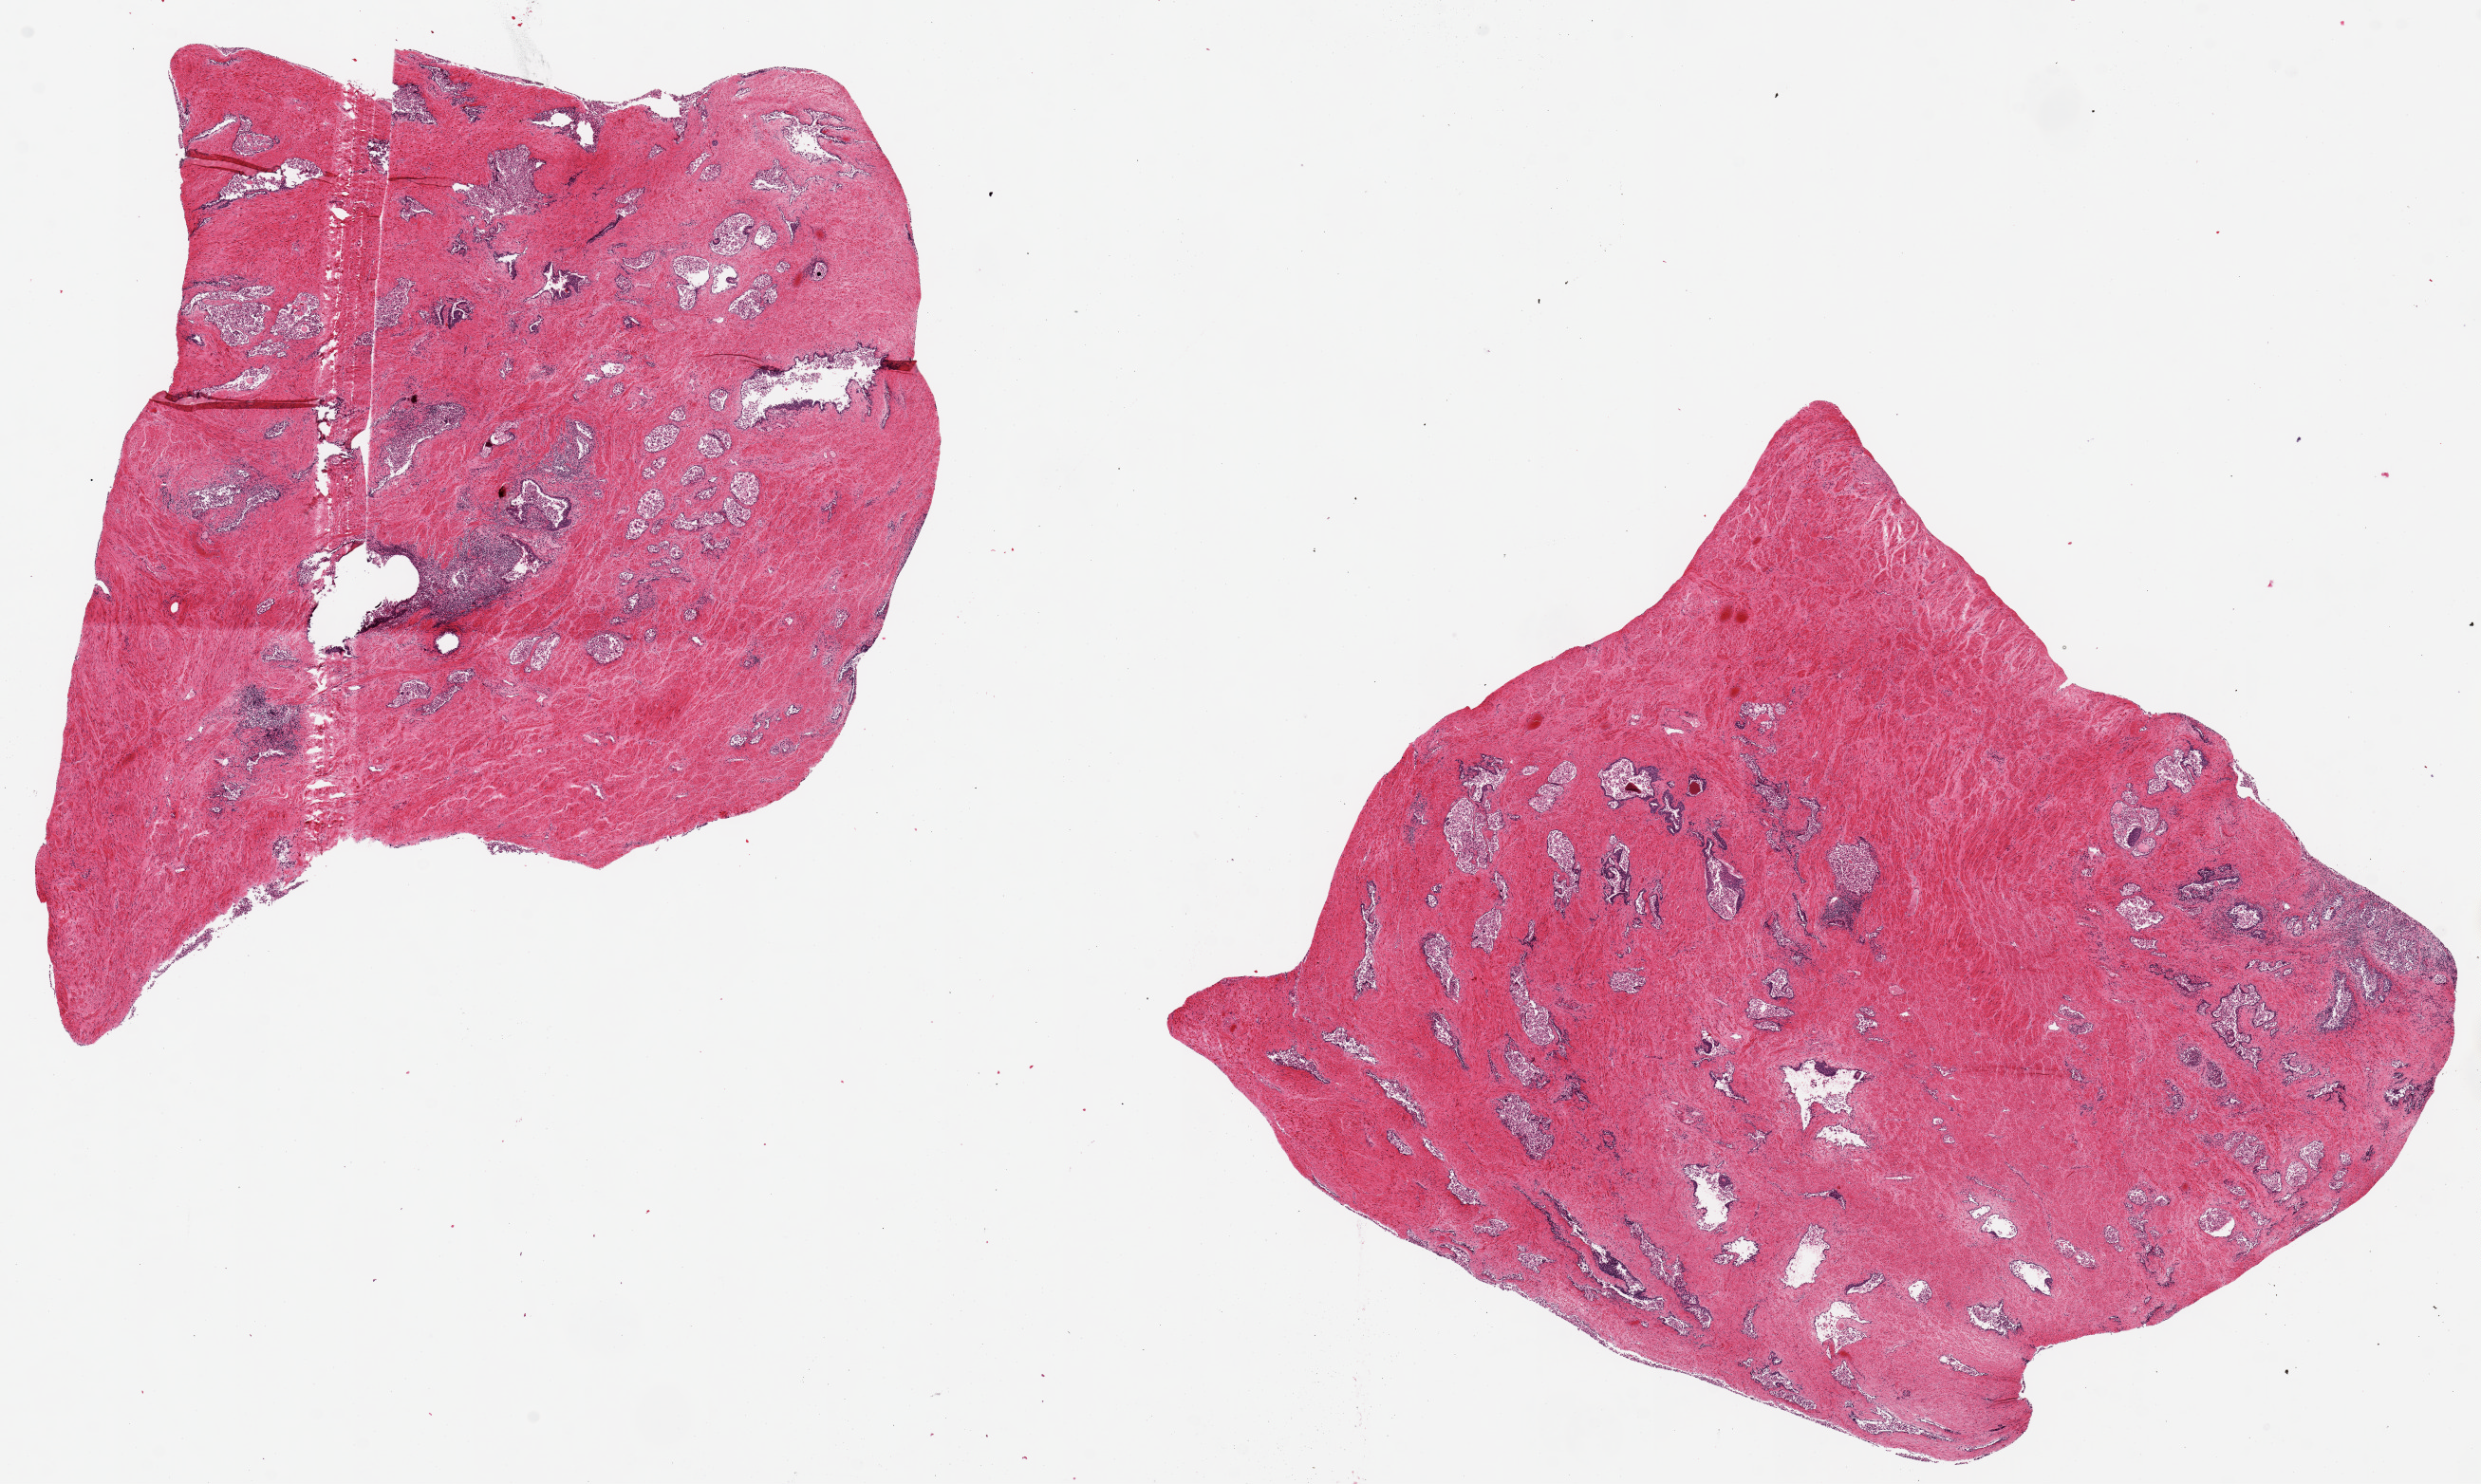
Digitized hematoxylin and eosin (H&E)-stained section, brightfield, a low-resolution overview of the entire scanned area, about 20.7 x 12.4 mm (acquisition: 20x scan), PAXgene-fixed paraffin-embedded (PFPE) section, section of prostate (target tissue), tissue donor sample. Donor sex: male.
Reviewer comment on this tissue sample: 2 pieces ~7x7mm; patchy marked chronic prostatitis; badly autolyzed glandular elements.